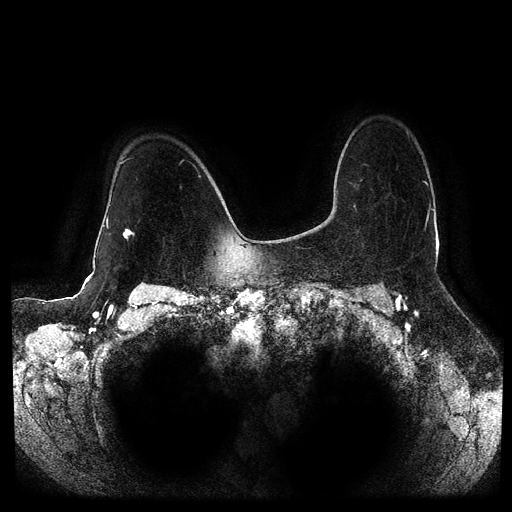
Breast MRI (dynamic contrast-enhanced, multi-phase), one axial slice. Position 75 of 116 along the scan axis. Dynamic contrast-enhanced series, time point 2 of 5 at this slice position (early post-contrast). 1.5 T. TE 2.6 ms, TR 5.2 ms. 512 × 512 image matrix. Female patient, age 53 years.
Structures marked on this image (semi-automatically segmented with operator editing):
- breast lesion (labelled 'tumour' in the annotation; benign lesions carry a separate 'benign' label): bounding box <122,228,134,241> (left, top, right, bottom; pixels)